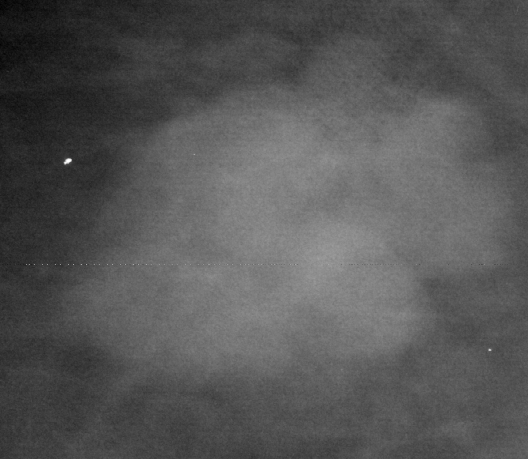
Region of interest cut from a scanned film mammogram (one marked finding); right breast; MLO view.
Mass, shape lobulated, margins microlobulated; BI-RADS assessment category 5; pathology (as recorded): malignant.